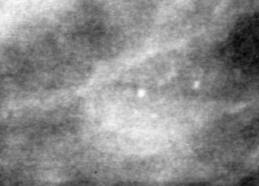
Region of interest cut from a scanned film mammogram (one marked finding); left breast; MLO view.
Marked abnormality: calcifications, morphology pleomorphic, distribution clustered; BI-RADS assessment category 4; pathology (as recorded): benign.